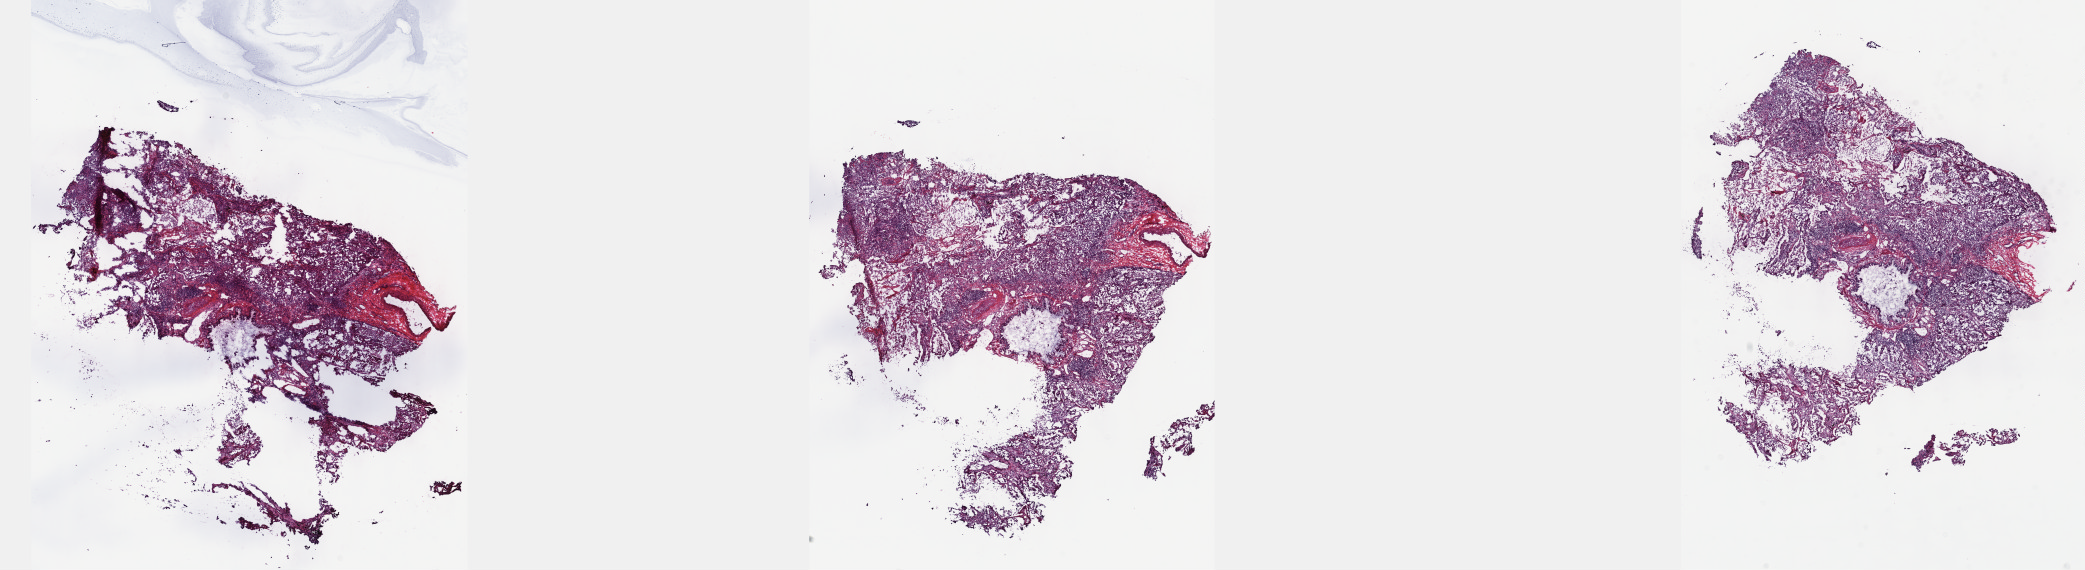
Digitized H&E tissue section (whole slide), a low-resolution overview of the entire scanned area, about 33.7 x 9.2 mm (slide scanned at 40x); frozen section from the top of the tissue portion; primary tumour sample from the lung. Female, age 39 years at initial diagnosis. Composition of this section per pathologist review: tumour cells 65%, tumour nuclei 65%, normal cells 3%, stromal cells 30%, necrosis 2%. Inflammatory infiltration, as recorded: lymphocyte infiltration 3%, monocyte infiltration 3%, neutrophil infiltration 6%.
Histologic diagnosis: Papillary adenocarcinoma, NOS (upper lobe, lung). AJCC pathologic stage: IA (6th edition).